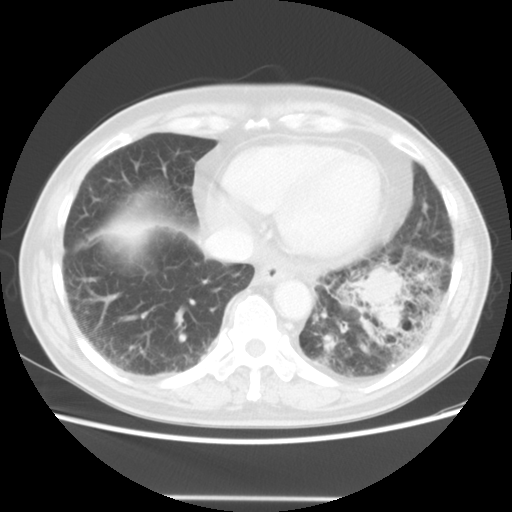
Chest CT, one axial slice; slice 13 of 56 in the series (ordered by position); lung window (W 1500 / L -600 HU); 512 × 512 image matrix. Male patient, age 66 years. From the clinical record (not read from this slice): clinical TNM (as recorded): T4 N3 M0; histopathological grade: G3.
Structures marked on this image (bounding box drawn by a radiologist):
- lung tumour (recorded histology: small cell carcinoma): bounding box [x1, y1, x2, y2] px = [351, 256, 410, 335]